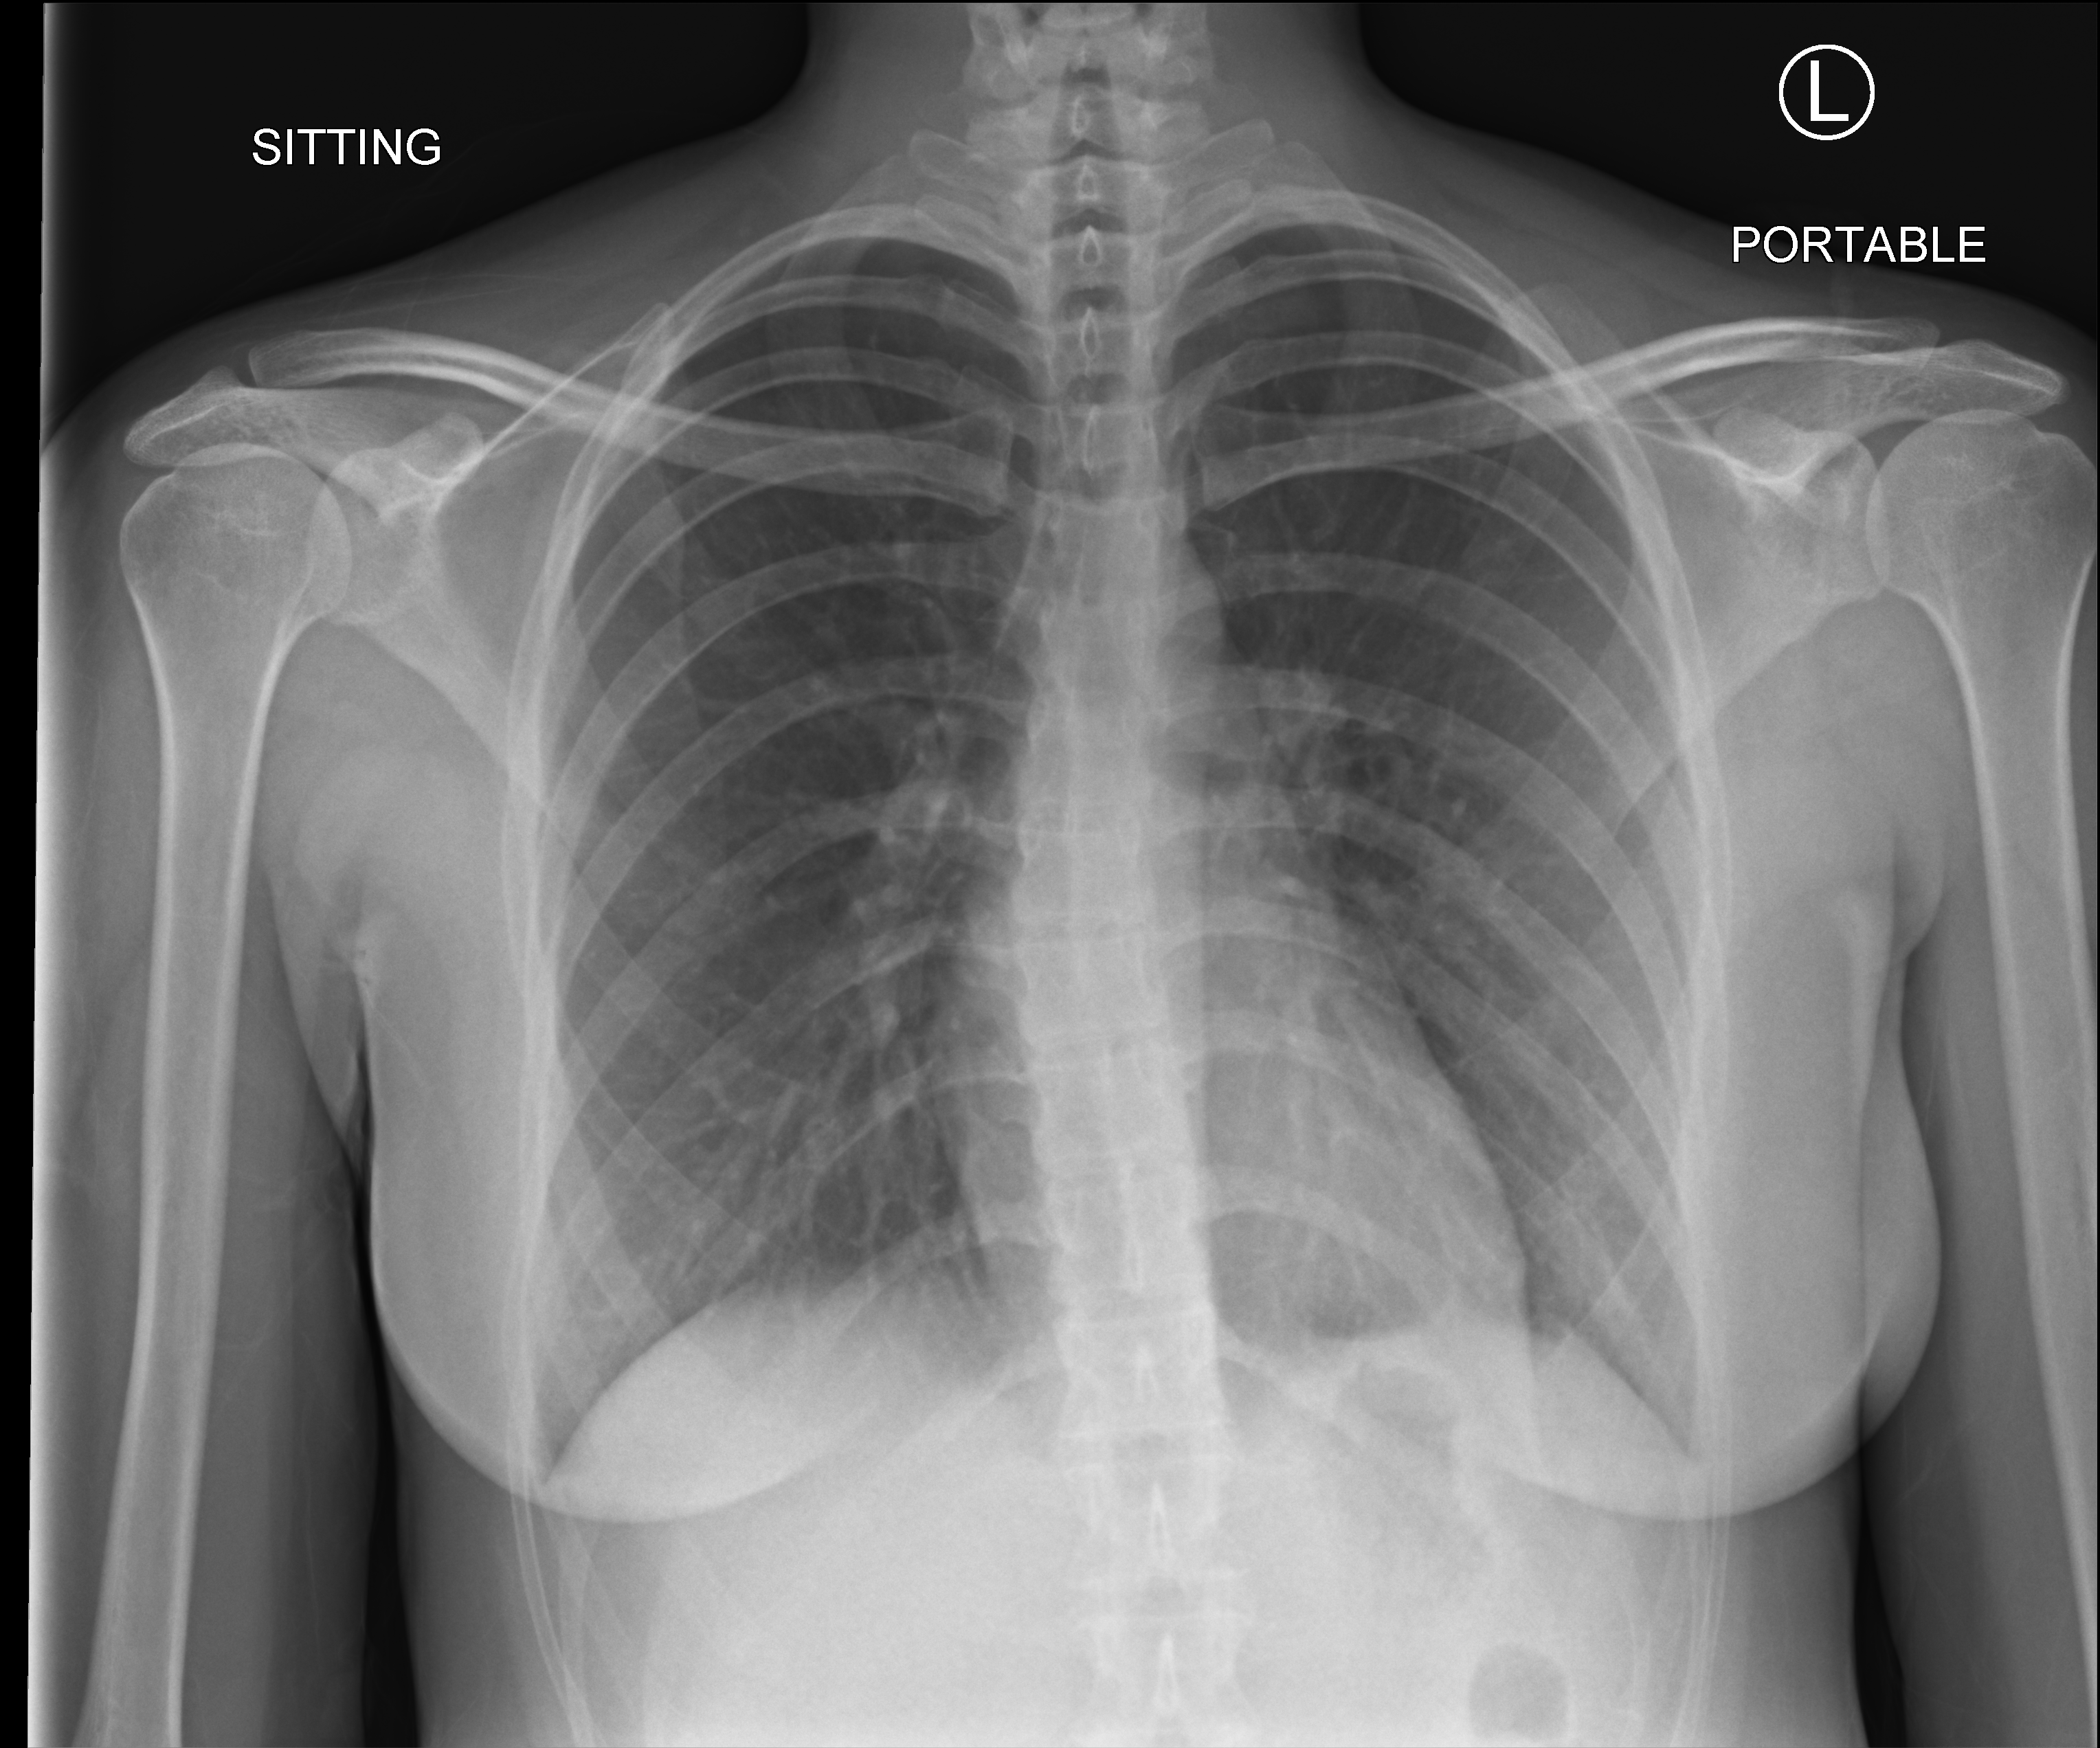
Bedside chest radiograph (computed radiography), anteroposterior (AP) projection. Patient hospitalised with COVID-19; female, aged 18–59 years.
From the hospital-stay record, not from the radiograph (when in the stay this image was taken is not recorded):
- mechanically ventilated during this hospital stay: no